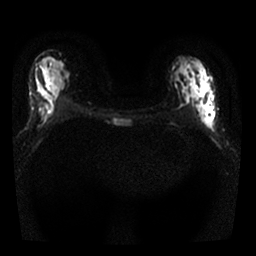
Breast MRI, one axial slice. Position 12 of 25 along the scan axis. Diffusion-weighted series; image 2 of 4 stored at this slice position (different b-values; order by instance number). 1.5 T. 256 × 256 image matrix, field of view 300 × 300 mm. Female patient.
Annotated regions visible in this slice (outlined manually by an expert reader):
- tumour on diffusion-weighted imaging: bounding box (x1, y1, x2, y2) in pixels: (193, 93, 217, 132)